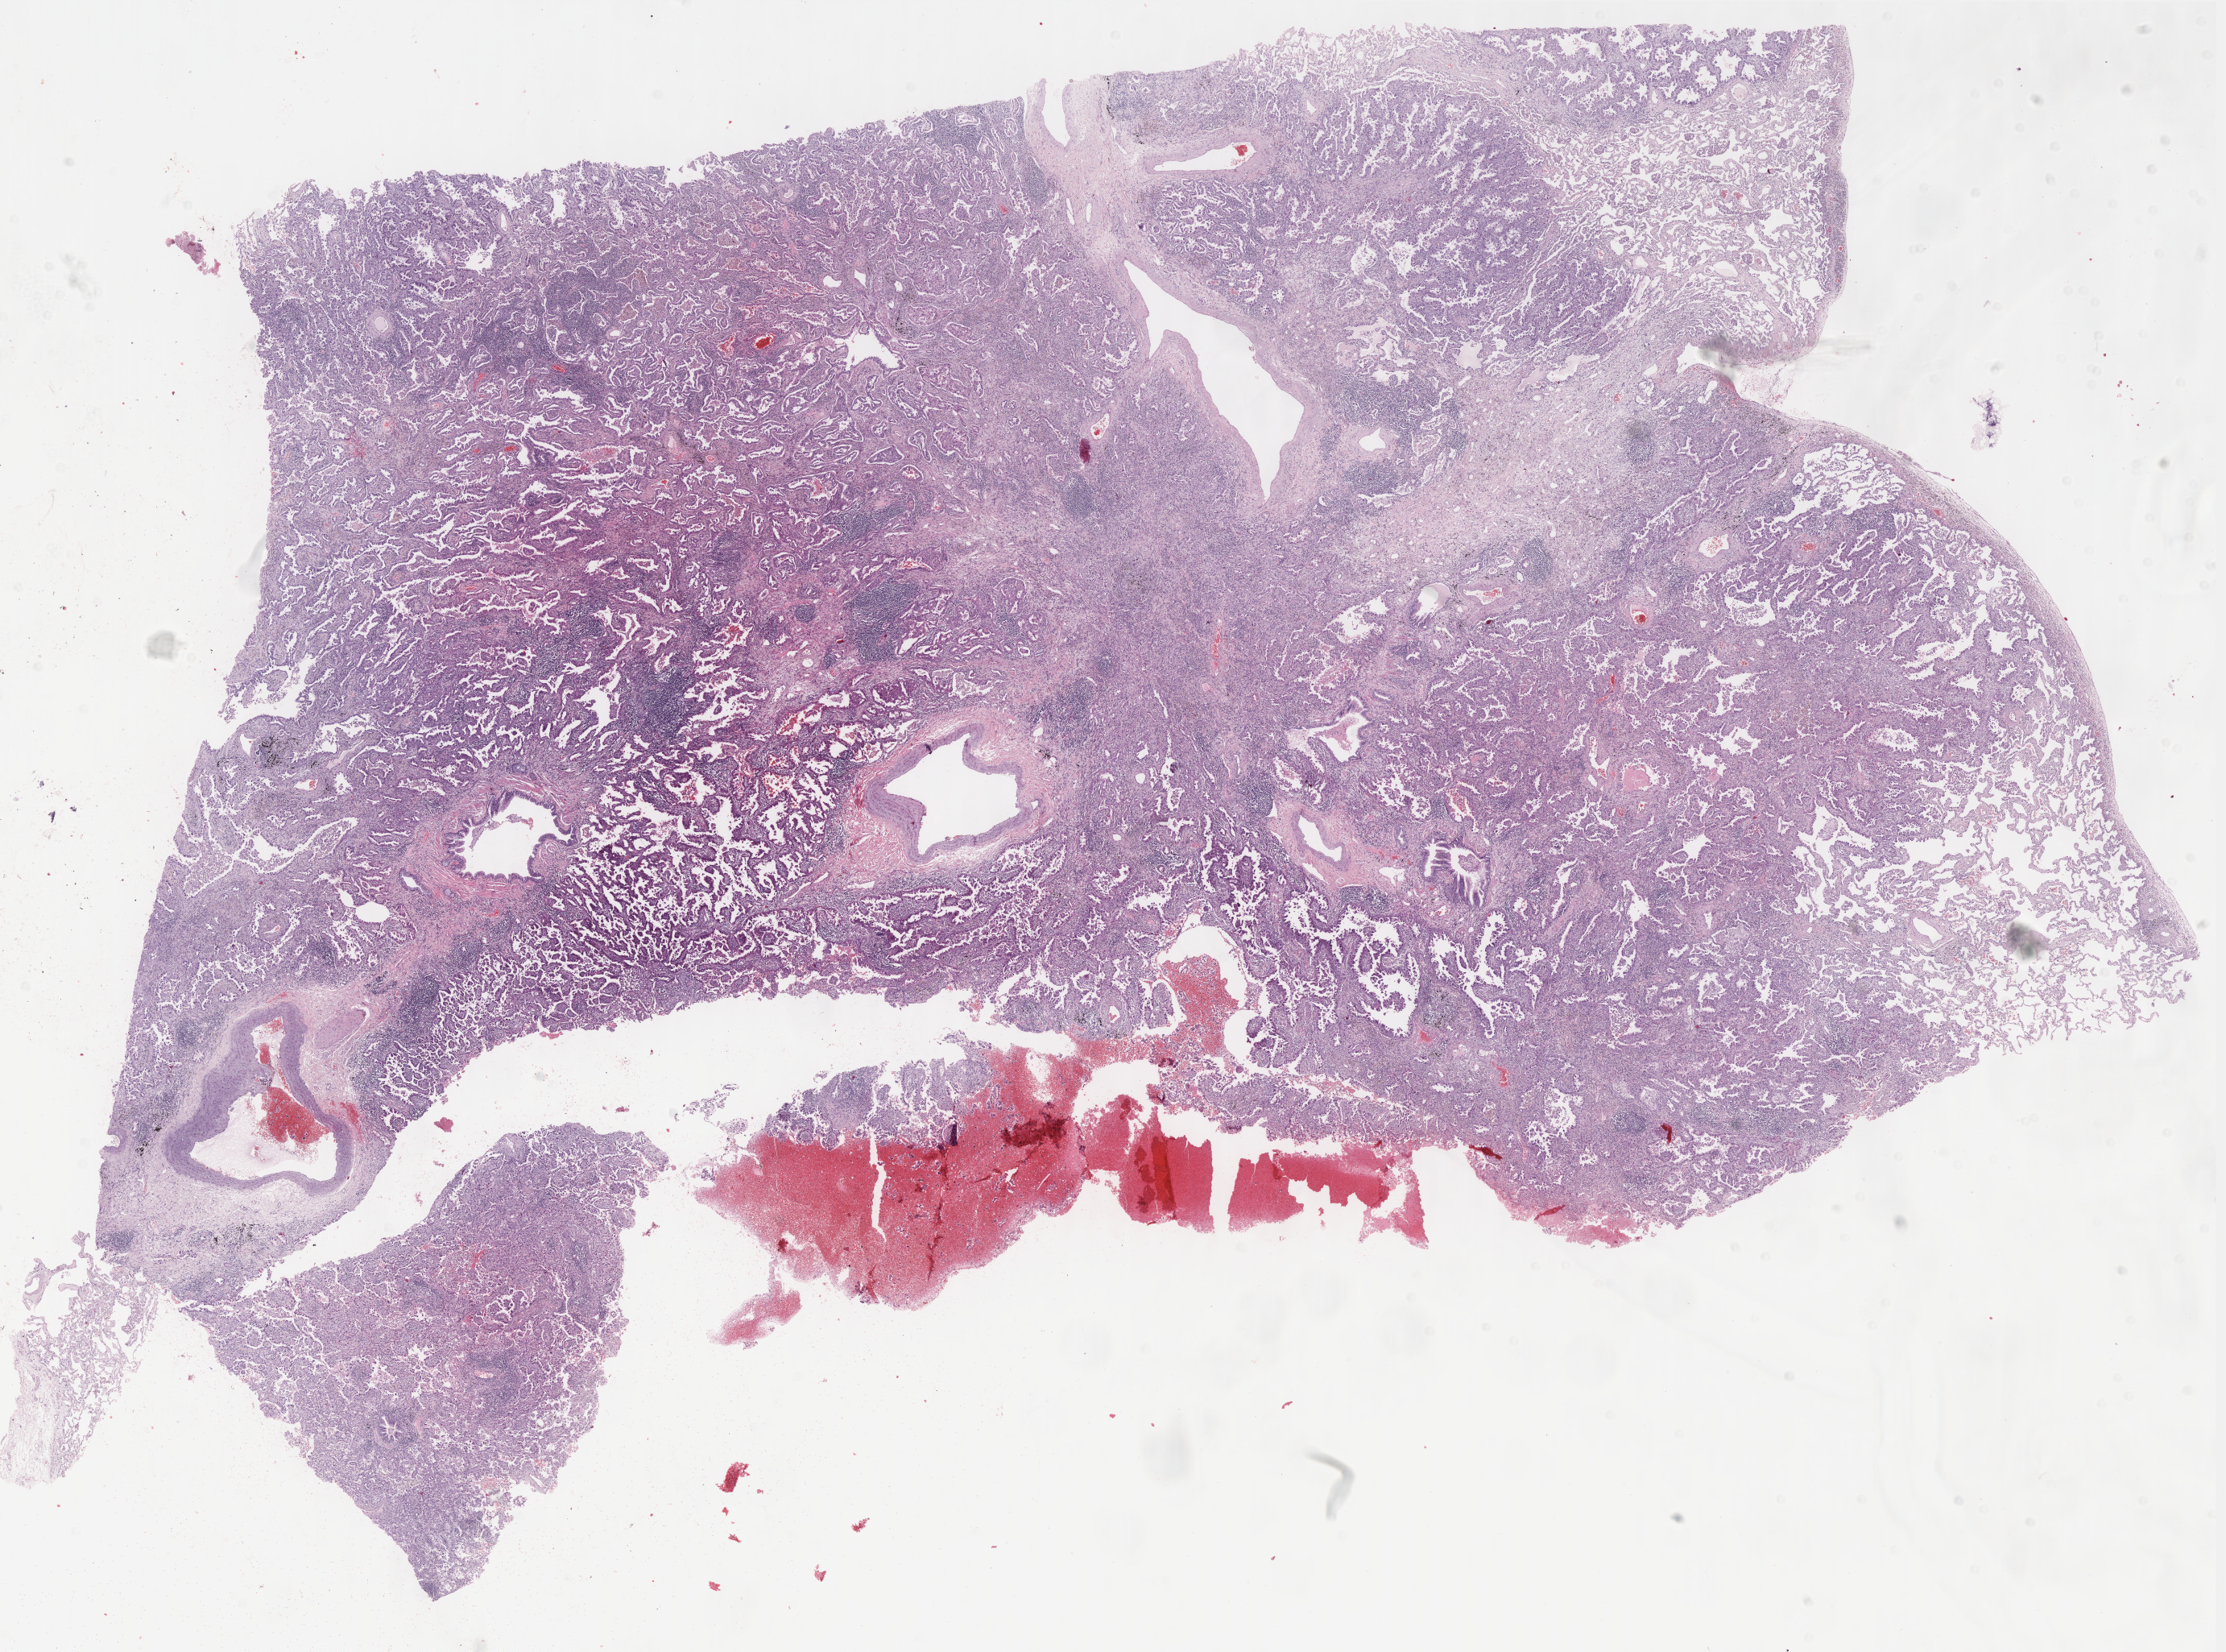
Whole-slide histology image, H&E-stained, a low-resolution overview of the entire scanned area, about 22.3 x 16.5 mm (slide scanned at 40x). FFPE section. Lung, primary tumour sample. Female, age 54 years at initial diagnosis.
Pathologic diagnosis: Adenocarcinoma with mixed subtypes (lower lobe, lung). Laterality: left. AJCC pathologic stage: IB (6th edition).